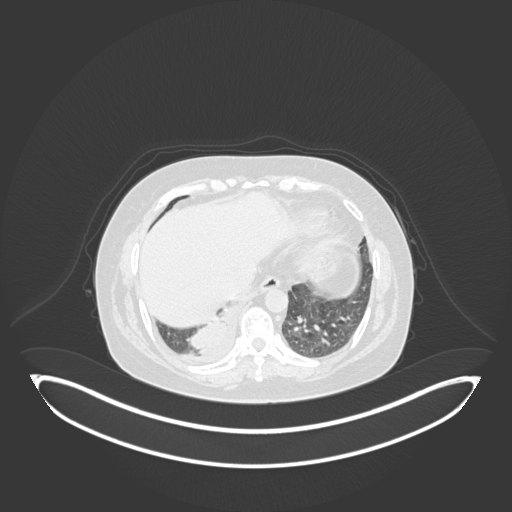
Chest CT, one axial slice; reconstruction kernel B30f; 120 kVp; lung window (W 1500 / L -600 HU); 512 × 512 image matrix, field of view 500 × 500 mm. Female patient, age 56 years. Case-level facts recorded for this patient, not image findings: clinical TNM (as recorded): T2b N1 M0; histopathological grade: G3.
Structures marked on this image (rectangle marked by the reading radiologist):
- lung tumour (recorded histology: small cell carcinoma): bounding box [x1, y1, x2, y2] px = [183, 303, 230, 357]